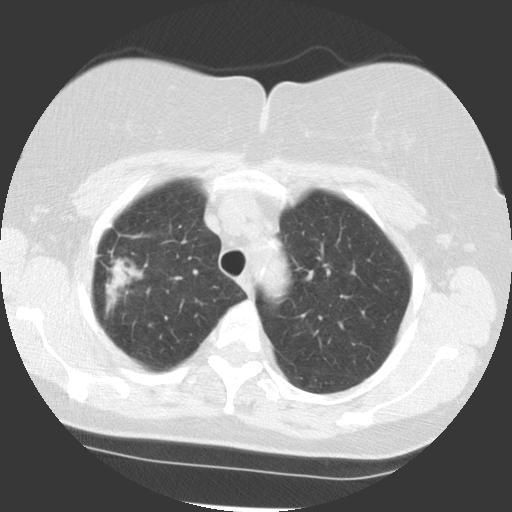
Low-dose screening chest CT, one axial slice; position 92 of 113 along the scan axis; lung window (W 1500 / L -600 HU); 512 × 512 image matrix, field of view 320 × 320 mm.
Structures marked on this image (manually delineated by an expert):
- lesion 1 (tumor, upper lobe of right lung): bounding box [x1, y1, x2, y2] px = [105, 258, 143, 312]